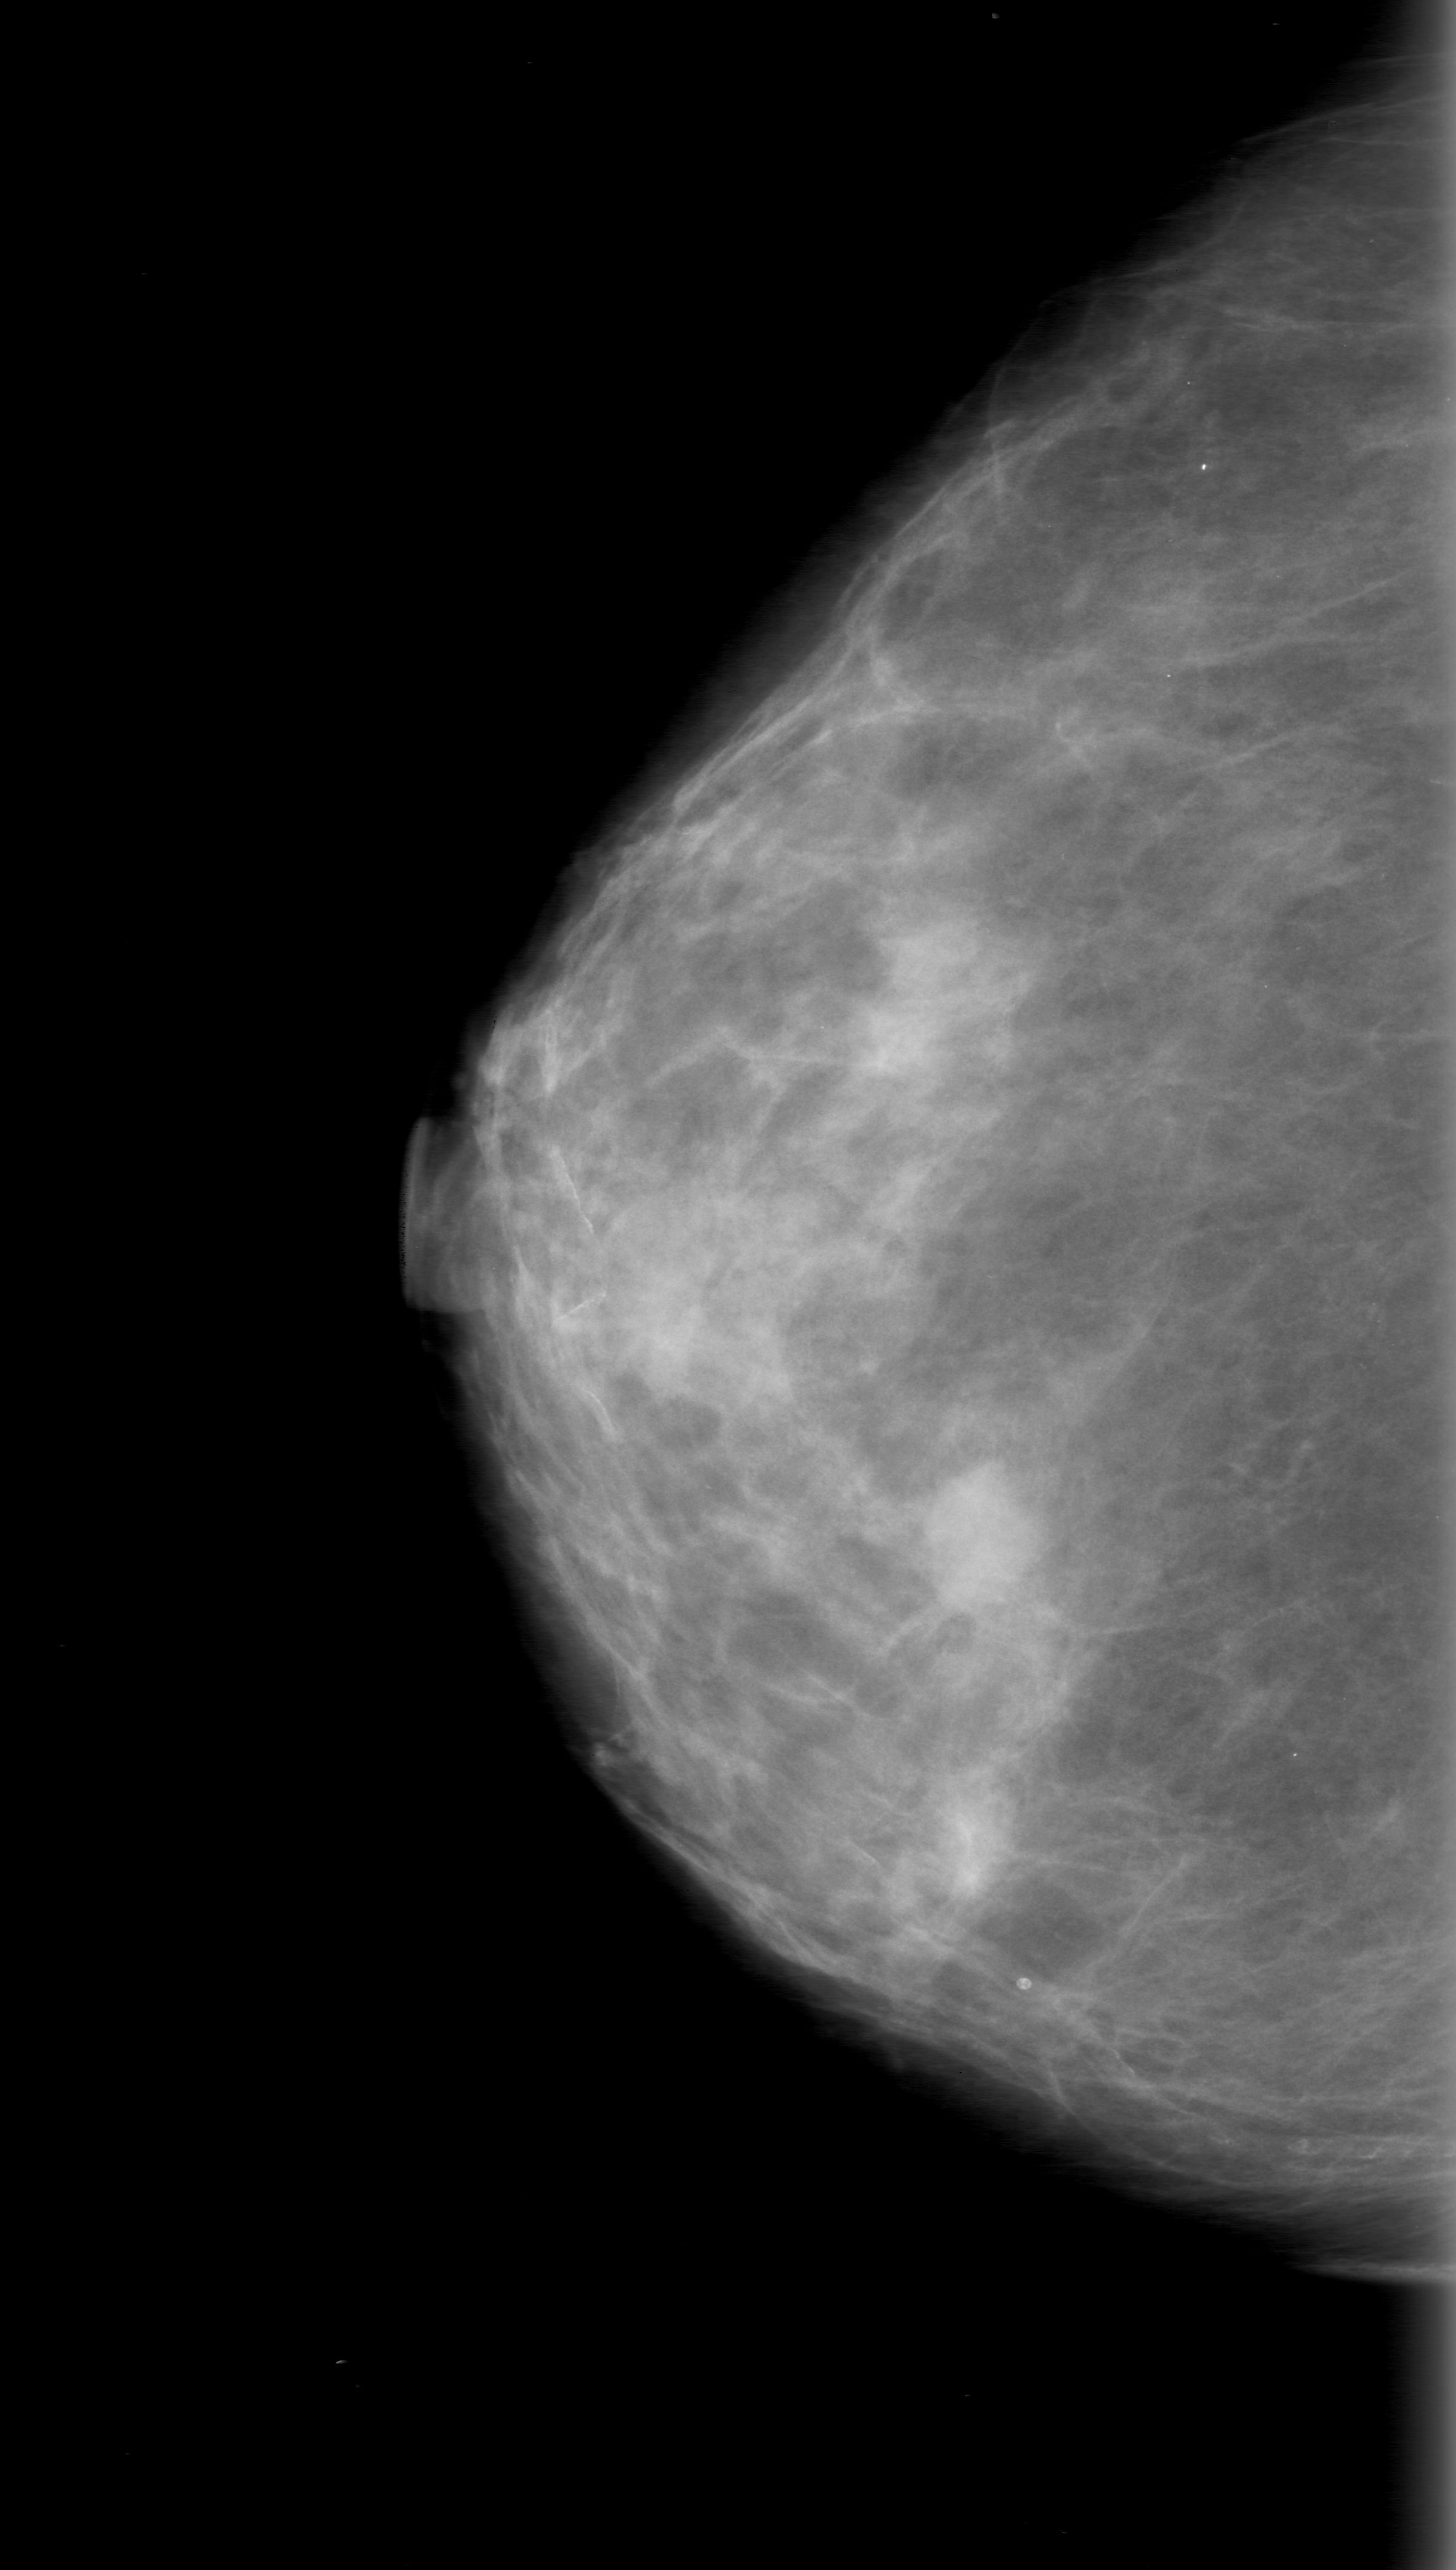
Mammogram (digitized film), right breast, craniocaudal (CC) view, breast composition: scattered fibroglandular densities (BI-RADS density category 2 of 4).
Finding: mass, shape oval, margins obscured; BI-RADS assessment category 0 (incomplete: needs additional imaging); subtlety rating 5 on a 1 (subtle) to 5 (obvious) scale; pathology (as recorded): benign.